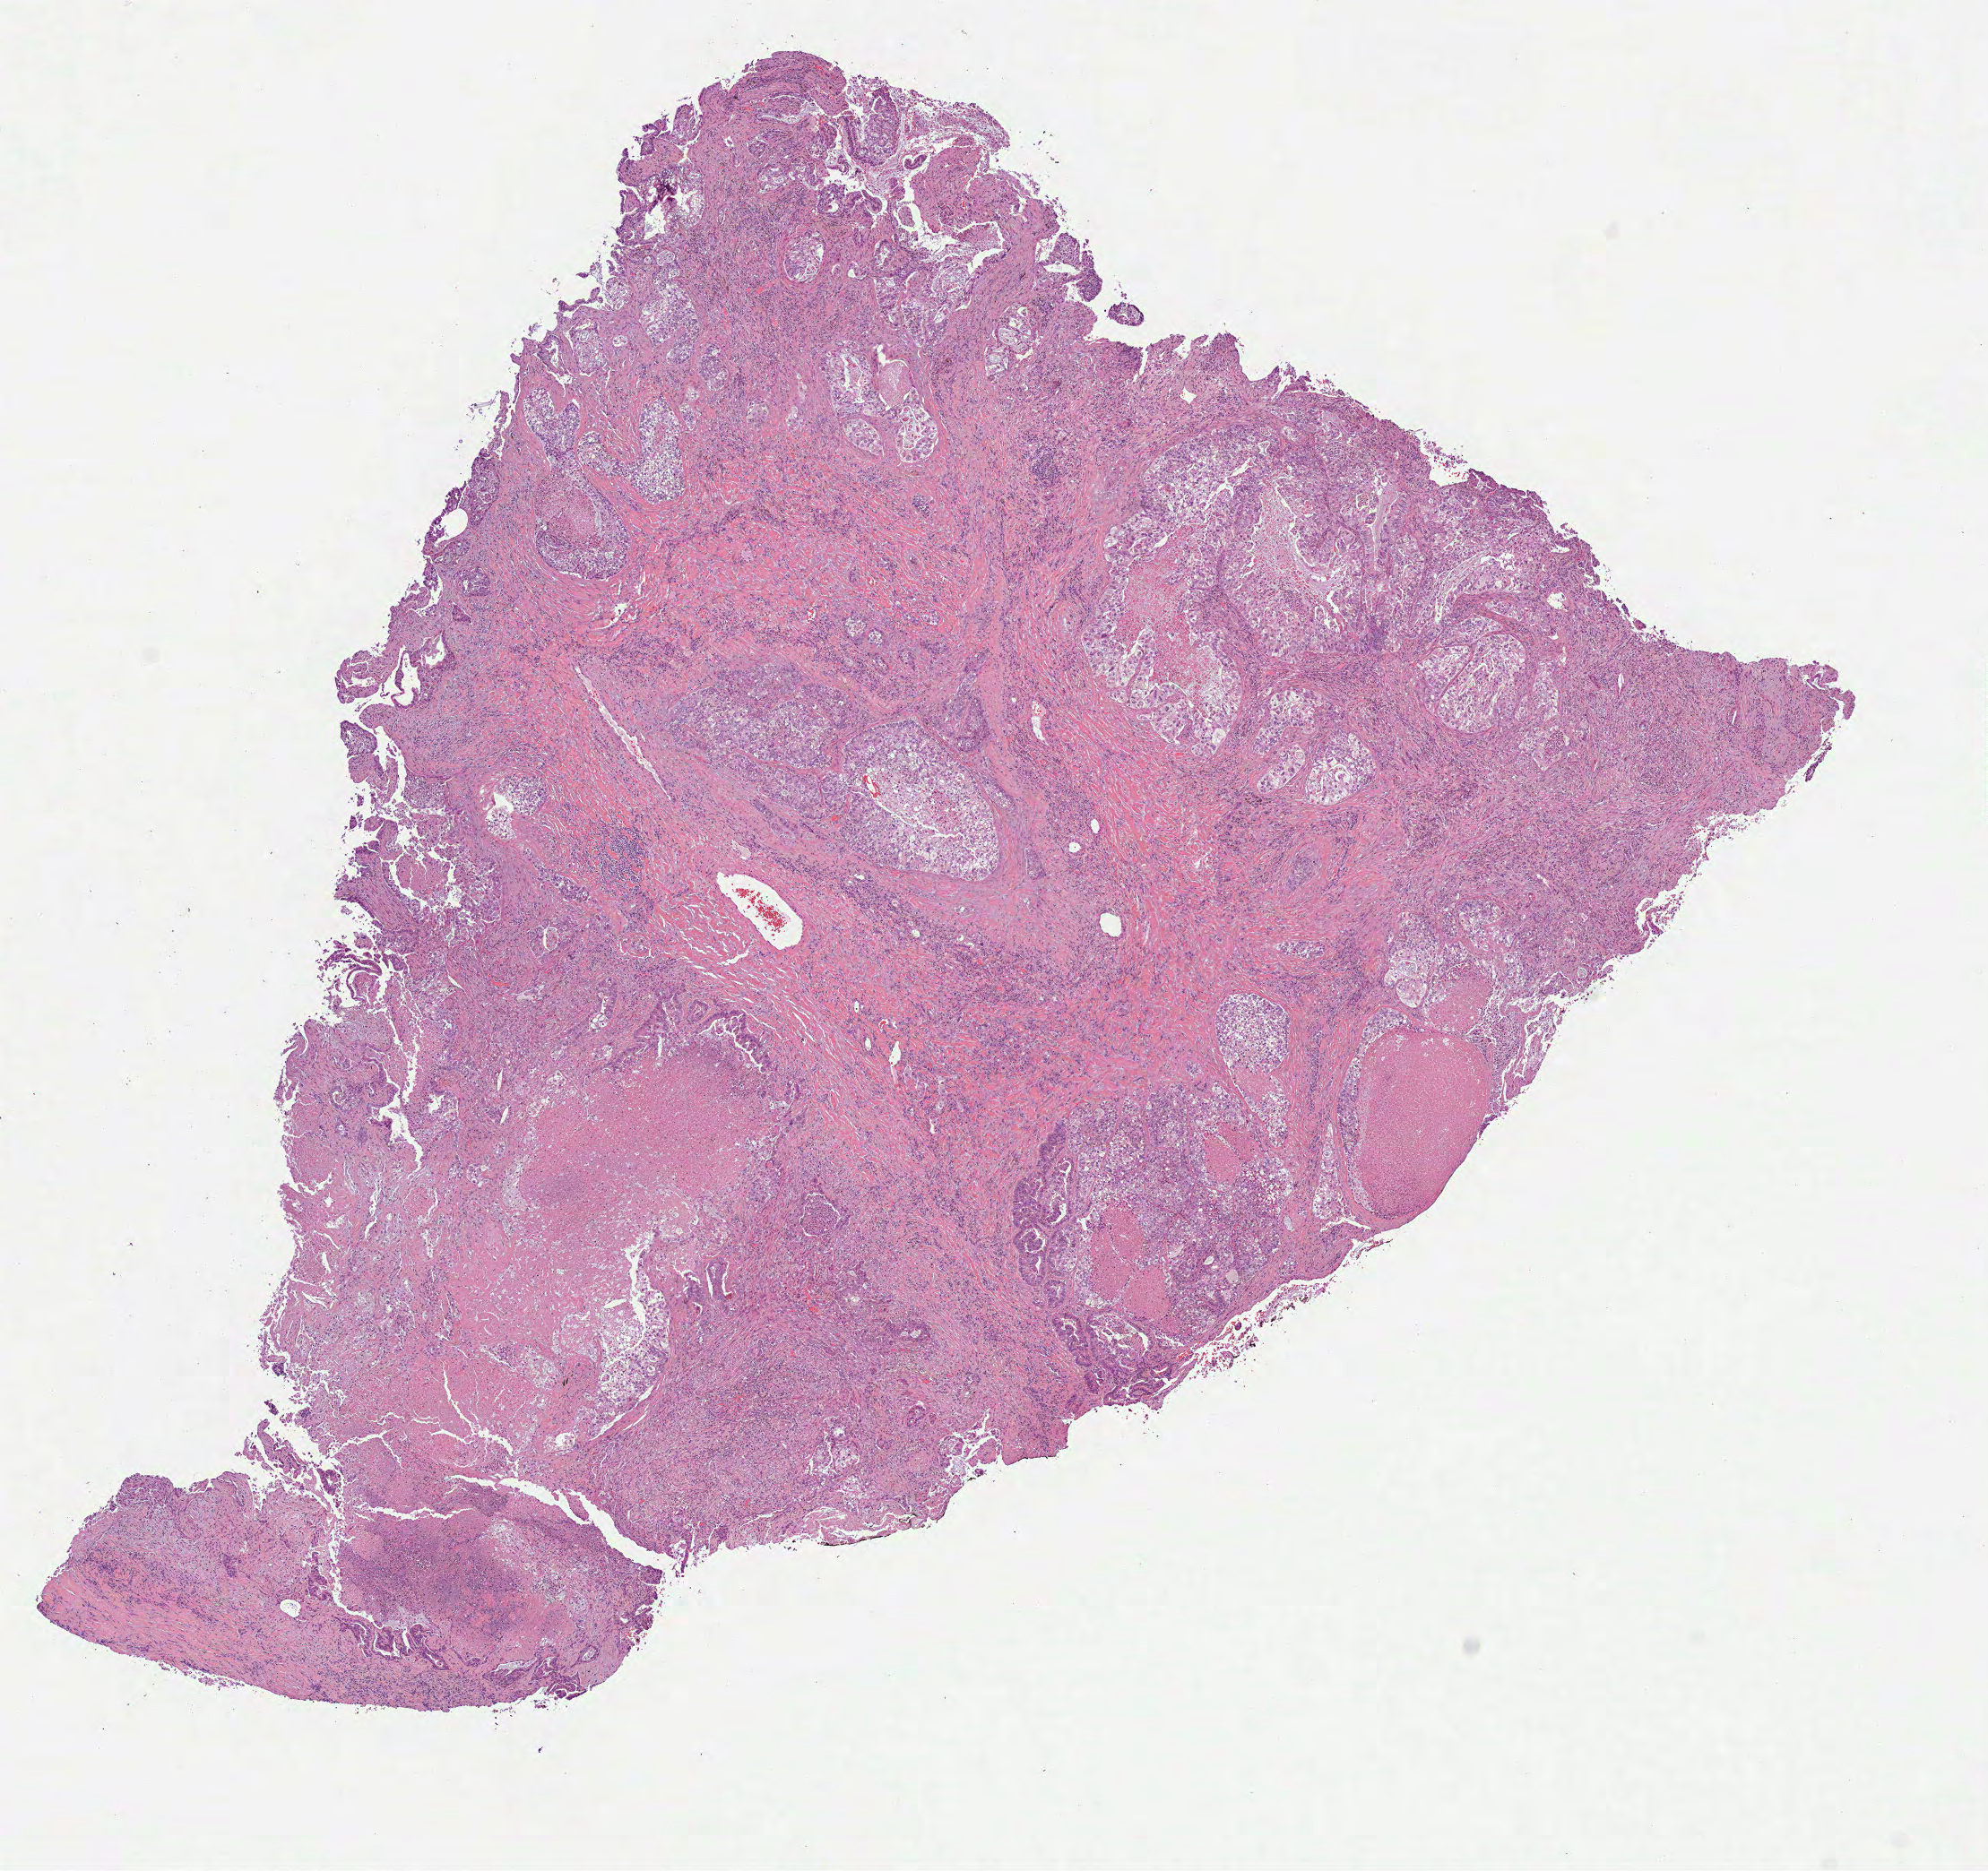
Digitized H&E tissue section (whole slide) — shown as a low-resolution overview of the whole scanned area (about 8.9 x 8.4 mm, acquisition: 40x scan); FFPE section; sample: primary tumour, lung. Male, age 61 years at initial diagnosis.
Pathologic diagnosis: Adenocarcinoma with mixed subtypes (lower lobe, lung). AJCC pathologic stage: IIB. Laterality: left.